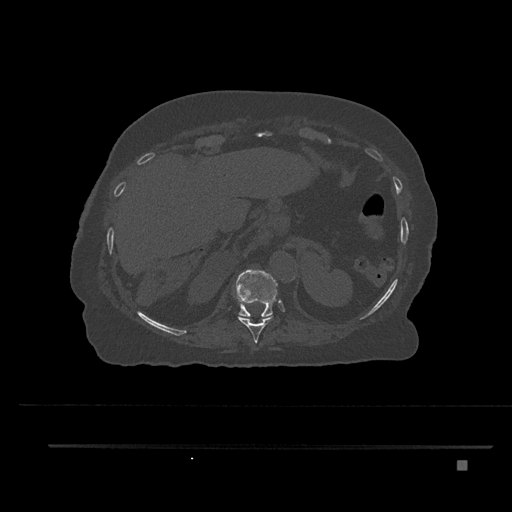
CT including the spine, one axial slice; slice 335 of 797 in the series (ordered by position); reconstruction kernel Br40s/3; bone window (W 1800 / L 400 HU); 0.5 mm slice thickness; 512 × 512 image matrix, field of view 437 × 437 mm. Patient: female, 76 years. From the clinical record (not read from this slice): primary cancer: lung.
Structures marked on this image (semi-automatic segmentation, software-assisted and operator-edited):
- T10 vertebra: bounding box [x1, y1, x2, y2] px = [238, 304, 273, 343]
- T11 vertebra: [233, 269, 278, 317]